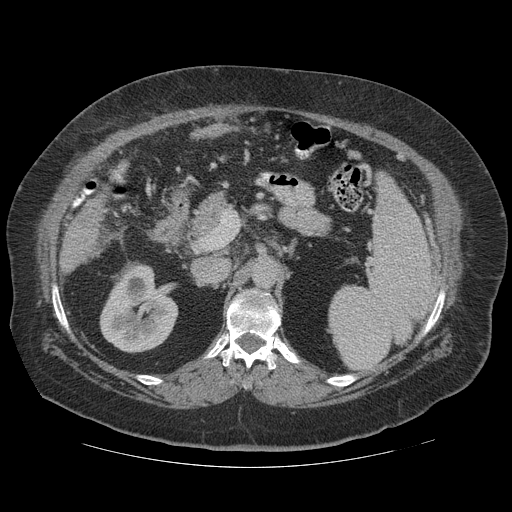
Contrast-enhanced abdominal CT (liver protocol), one axial slice; slice 57 of 121 in the series (ordered by position); reconstruction kernel STANDARD; soft-tissue window (W 400 / L 40 HU); 2.5 mm slice thickness; 512 × 512 image matrix, field of view 420 × 420 mm. From the clinical record (not read from this slice): diagnosis: hepatocellular carcinoma (patient treated with transarterial chemoembolisation; whether this scan precedes or follows treatment is not stated here); TNM stage (as recorded): Stage-IIIA; Child-Pugh class: A.
Annotated regions visible in this slice (semi-automatically segmented with operator editing):
- liver parenchyma outside the tumour (the mass and vessels are separate outlines, so this box may not span the whole liver): bounding box (x1, y1, x2, y2) in pixels: (60, 242, 78, 272)